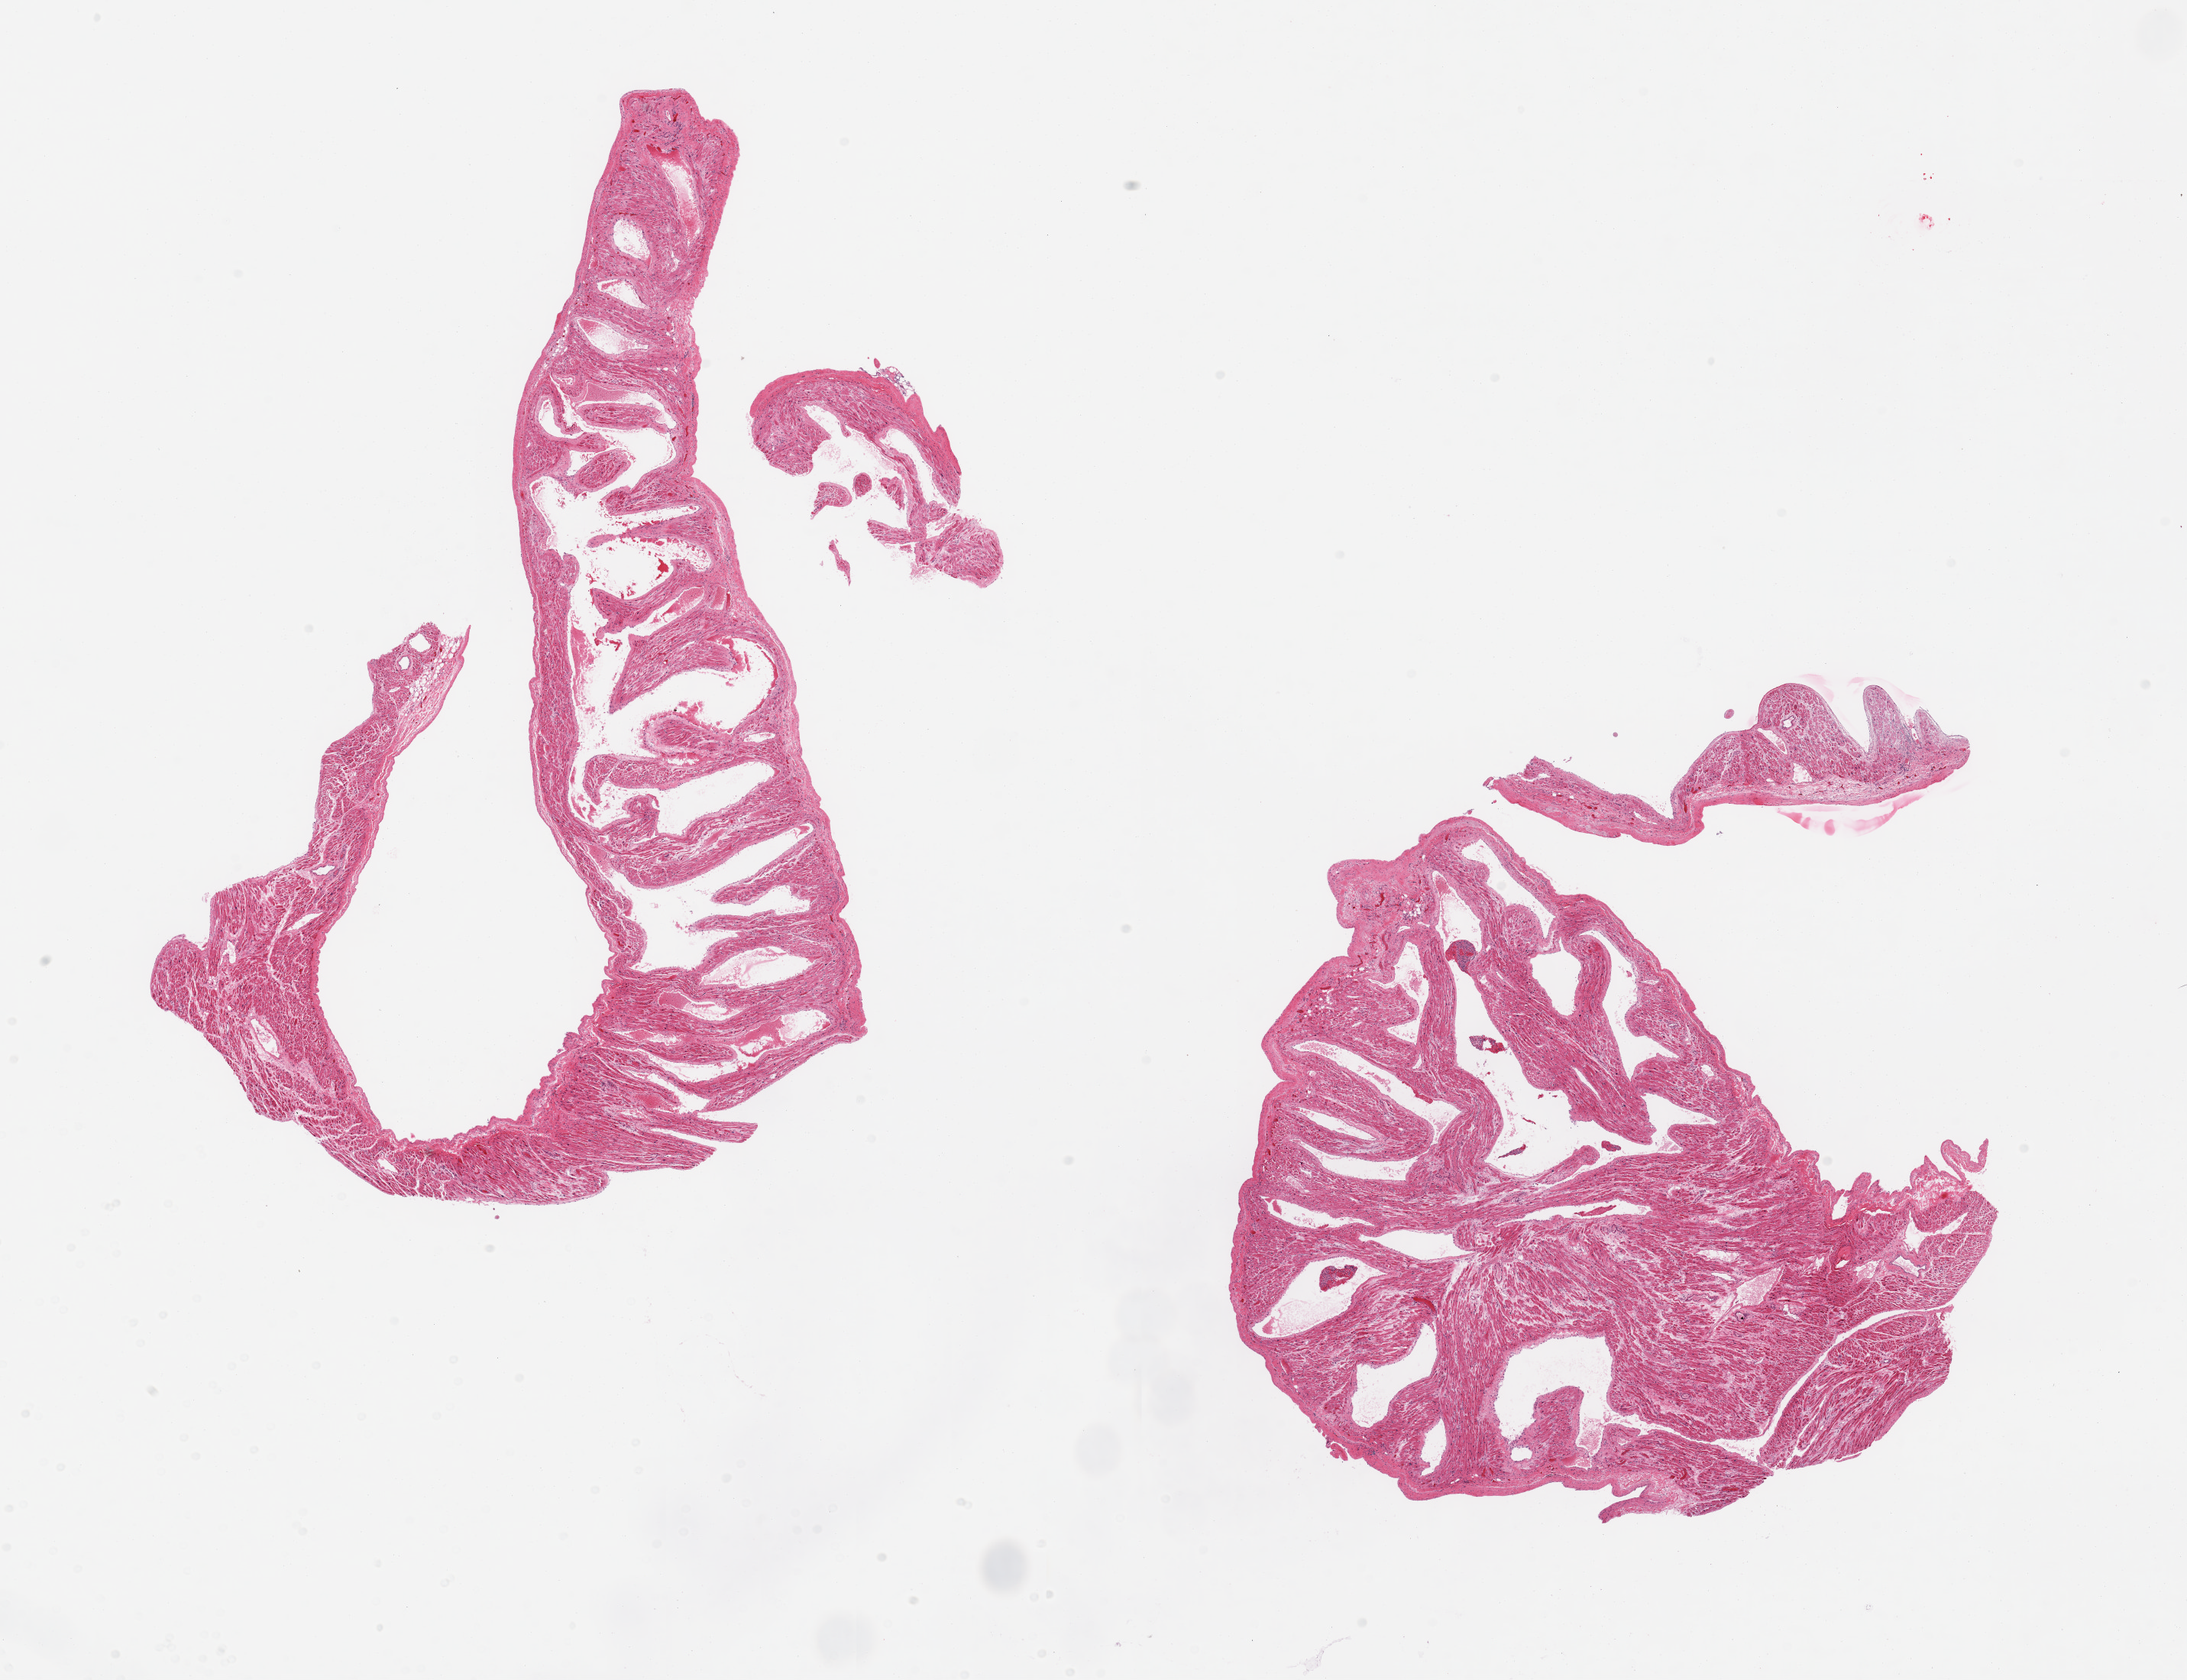
Whole-slide image, H&E stain — low-resolution overview of the scanned area, about 22.6 x 17.4 mm (from a 20x scan), PAXgene-fixed, paraffin-embedded tissue, sampled site (target tissue): auricular appendage, tissue donor sample. Donor sex: male.
• review note (as recorded): 2 pieces; congestion